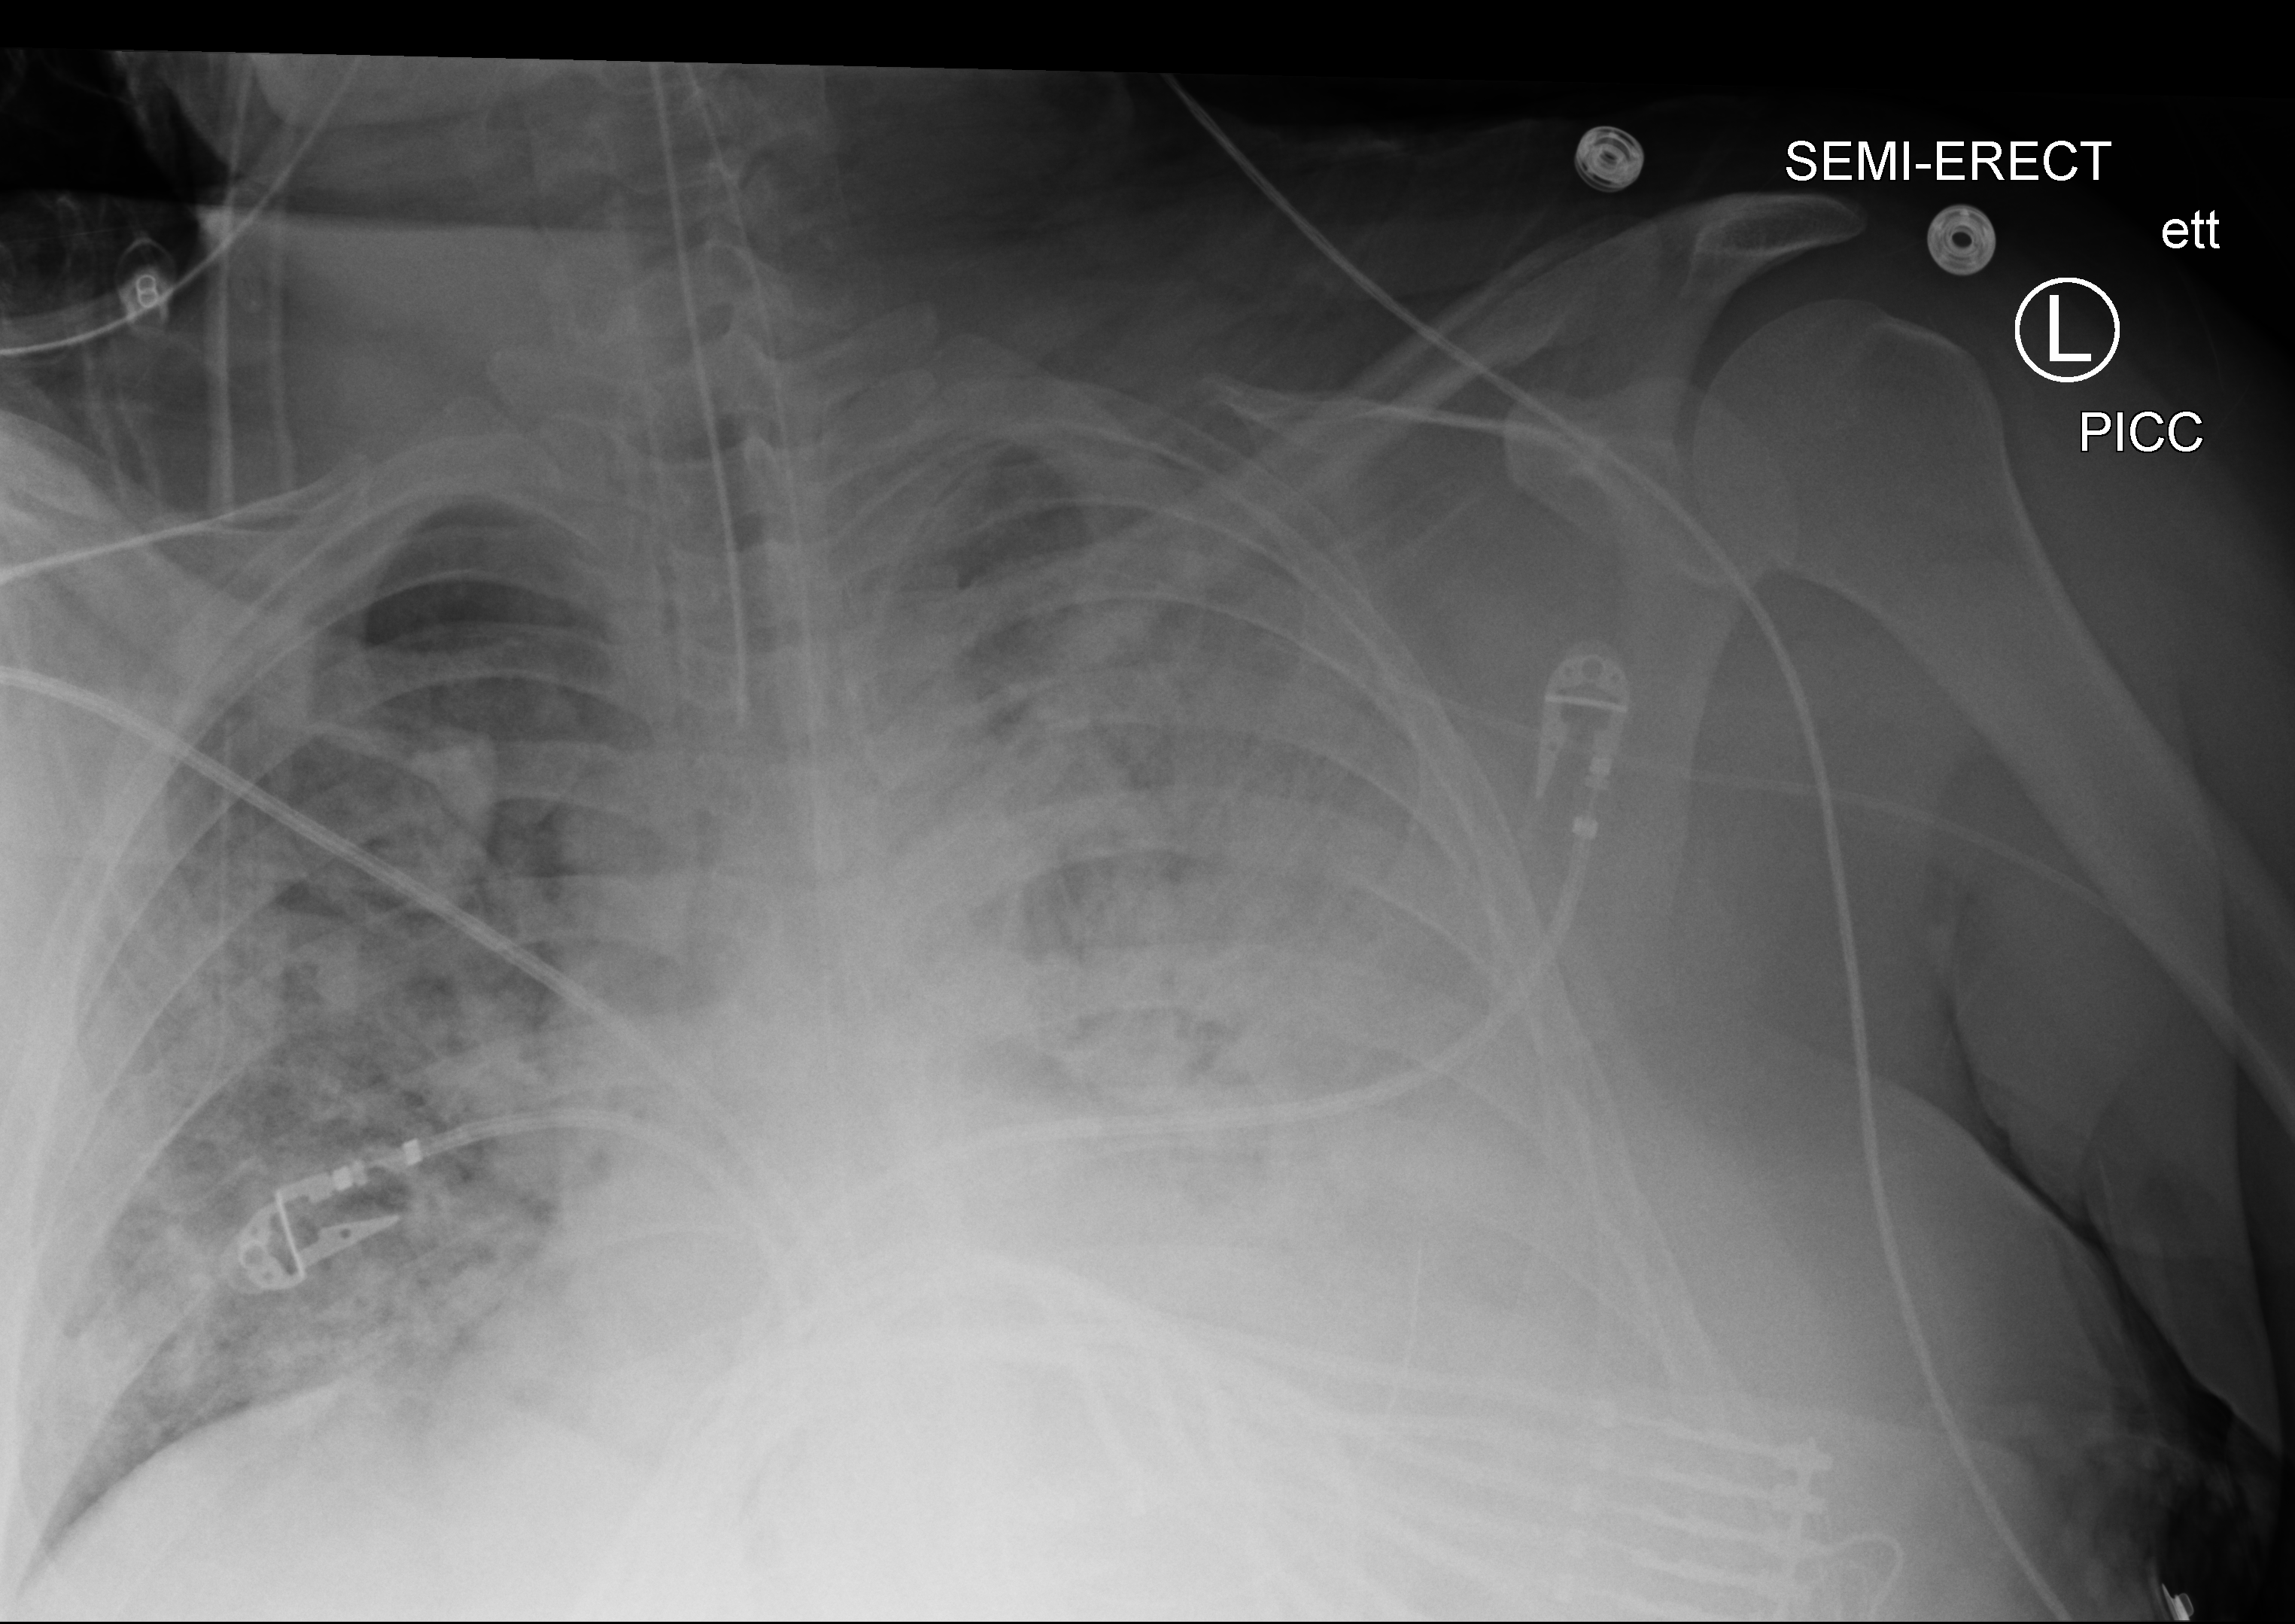
Chest X-ray (portable); anteroposterior (AP) projection. Adult patient hospitalised with COVID-19, age 18–59 years.
Hospital-stay facts (about this admission, not read from this image; timing relative to this image not recorded):
- length of hospital stay: 15 days
- mechanically ventilated during this hospital stay: yes
- admitted to intensive care during this hospital stay: yes